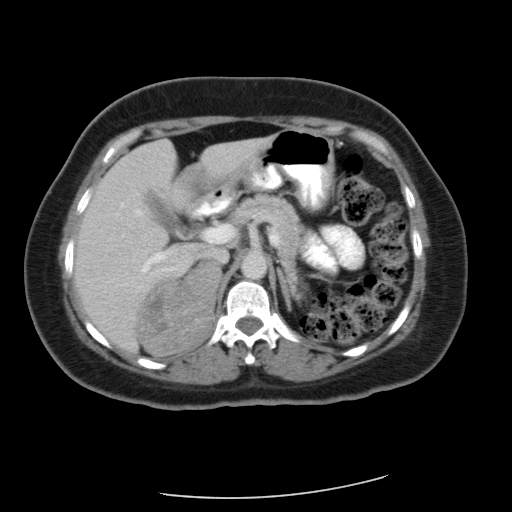
Contrast-enhanced abdominal CT, one axial slice; position 38 of 56 along the scan axis; soft-tissue window (W 400 / L 40 HU); 5 mm slice thickness; 512 × 512 image matrix. Patient: female, 58 years. Case-level facts recorded for this patient, not image findings: diagnosis: adrenocortical carcinoma; tumour side: right adrenal; tumour size at pathology: 9 cm; Ki-67 index: 25 %; stage (as recorded): 3.
Structures marked on this image (semi-automatically segmented with operator editing):
- mass: box from (x=138, y=264) to (x=218, y=356) px